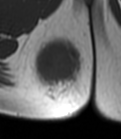
MRI of an extremity soft-tissue mass, one axial slice. Position 17 of 47 along the scan axis. MR volume resampled by the dataset authors to the PET/CT grid (not the native acquisition matrix). 121 × 139 image matrix, field of view 118 × 136 mm. Female patient. Case-level facts recorded for this patient, not image findings: histological type: epithelioid sarcoma; grade: intermediate; site of the primary tumour: right buttock.
Structures marked on this image (expert contour drawn on MRI and transferred to this co-registered scan by the dataset authors):
- gross tumour volume including surrounding oedema: box from (x=32, y=36) to (x=90, y=108) px
- gross tumour volume (mass): (x=36, y=43)–(x=78, y=83)